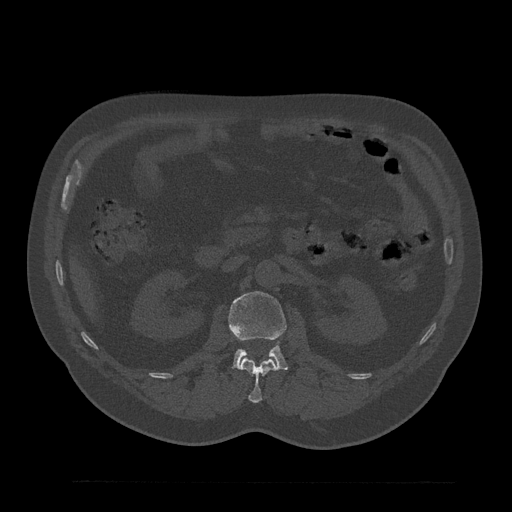
CT including the spine, one axial slice. Slice 129 of 797 in the series (ordered by position). Reconstruction kernel Br40s/3. 120 kVp. Bone window (W 1800 / L 400 HU). 512 × 512 image matrix, field of view 430 × 430 mm. Male patient, age 61 years. From the clinical record (not read from this slice): primary cancer: prostate.
Outlined on this slice (semi-automatic segmentation, software-assisted and operator-edited):
- L1 vertebra: box from (x=240, y=358) to (x=279, y=403) px
- L2 vertebra: (x=228, y=291)–(x=288, y=370)